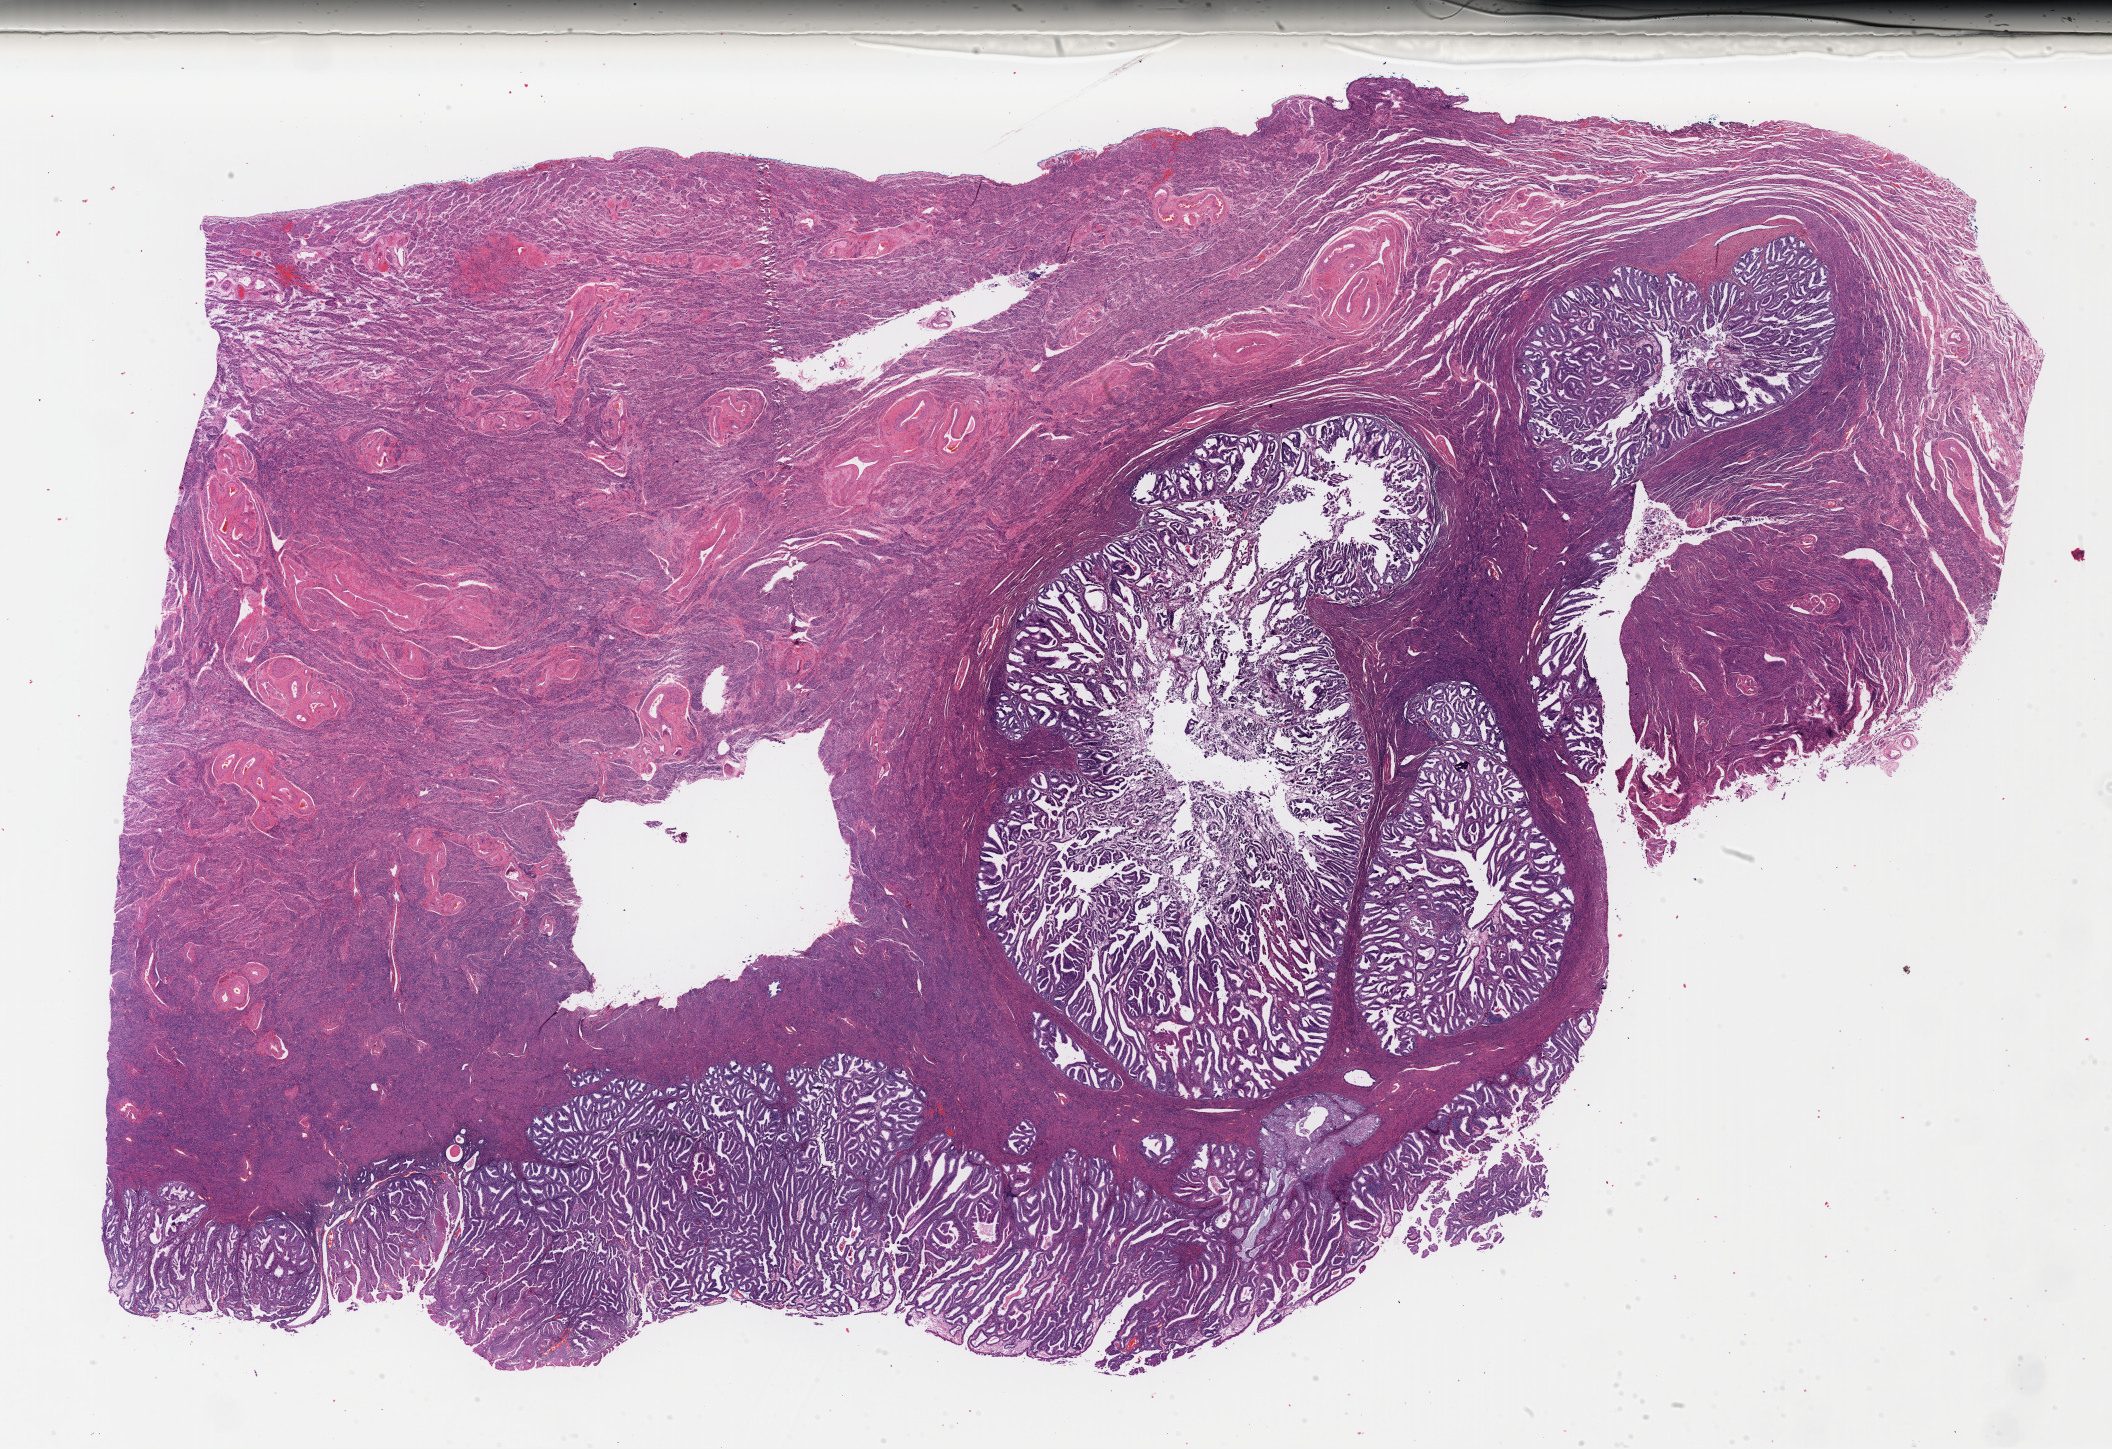
Digitized Hematoxylin and eosin (H&E) stained tissue section (whole slide), shown as a low-resolution overview of the whole scanned area (about 33.2 x 22.8 mm); formalin-fixed paraffin-embedded (FFPE) diagnostic section; primary tumour sample from the uterus. Patient: female, age at initial diagnosis 71 years. Histologic grade: G2 (moderately differentiated).
FIGO stage: IC. Lymph nodes positive (case pathology): 0 of 9 examined. Pathologic diagnosis: Endometrioid adenocarcinoma, NOS (endometrium).